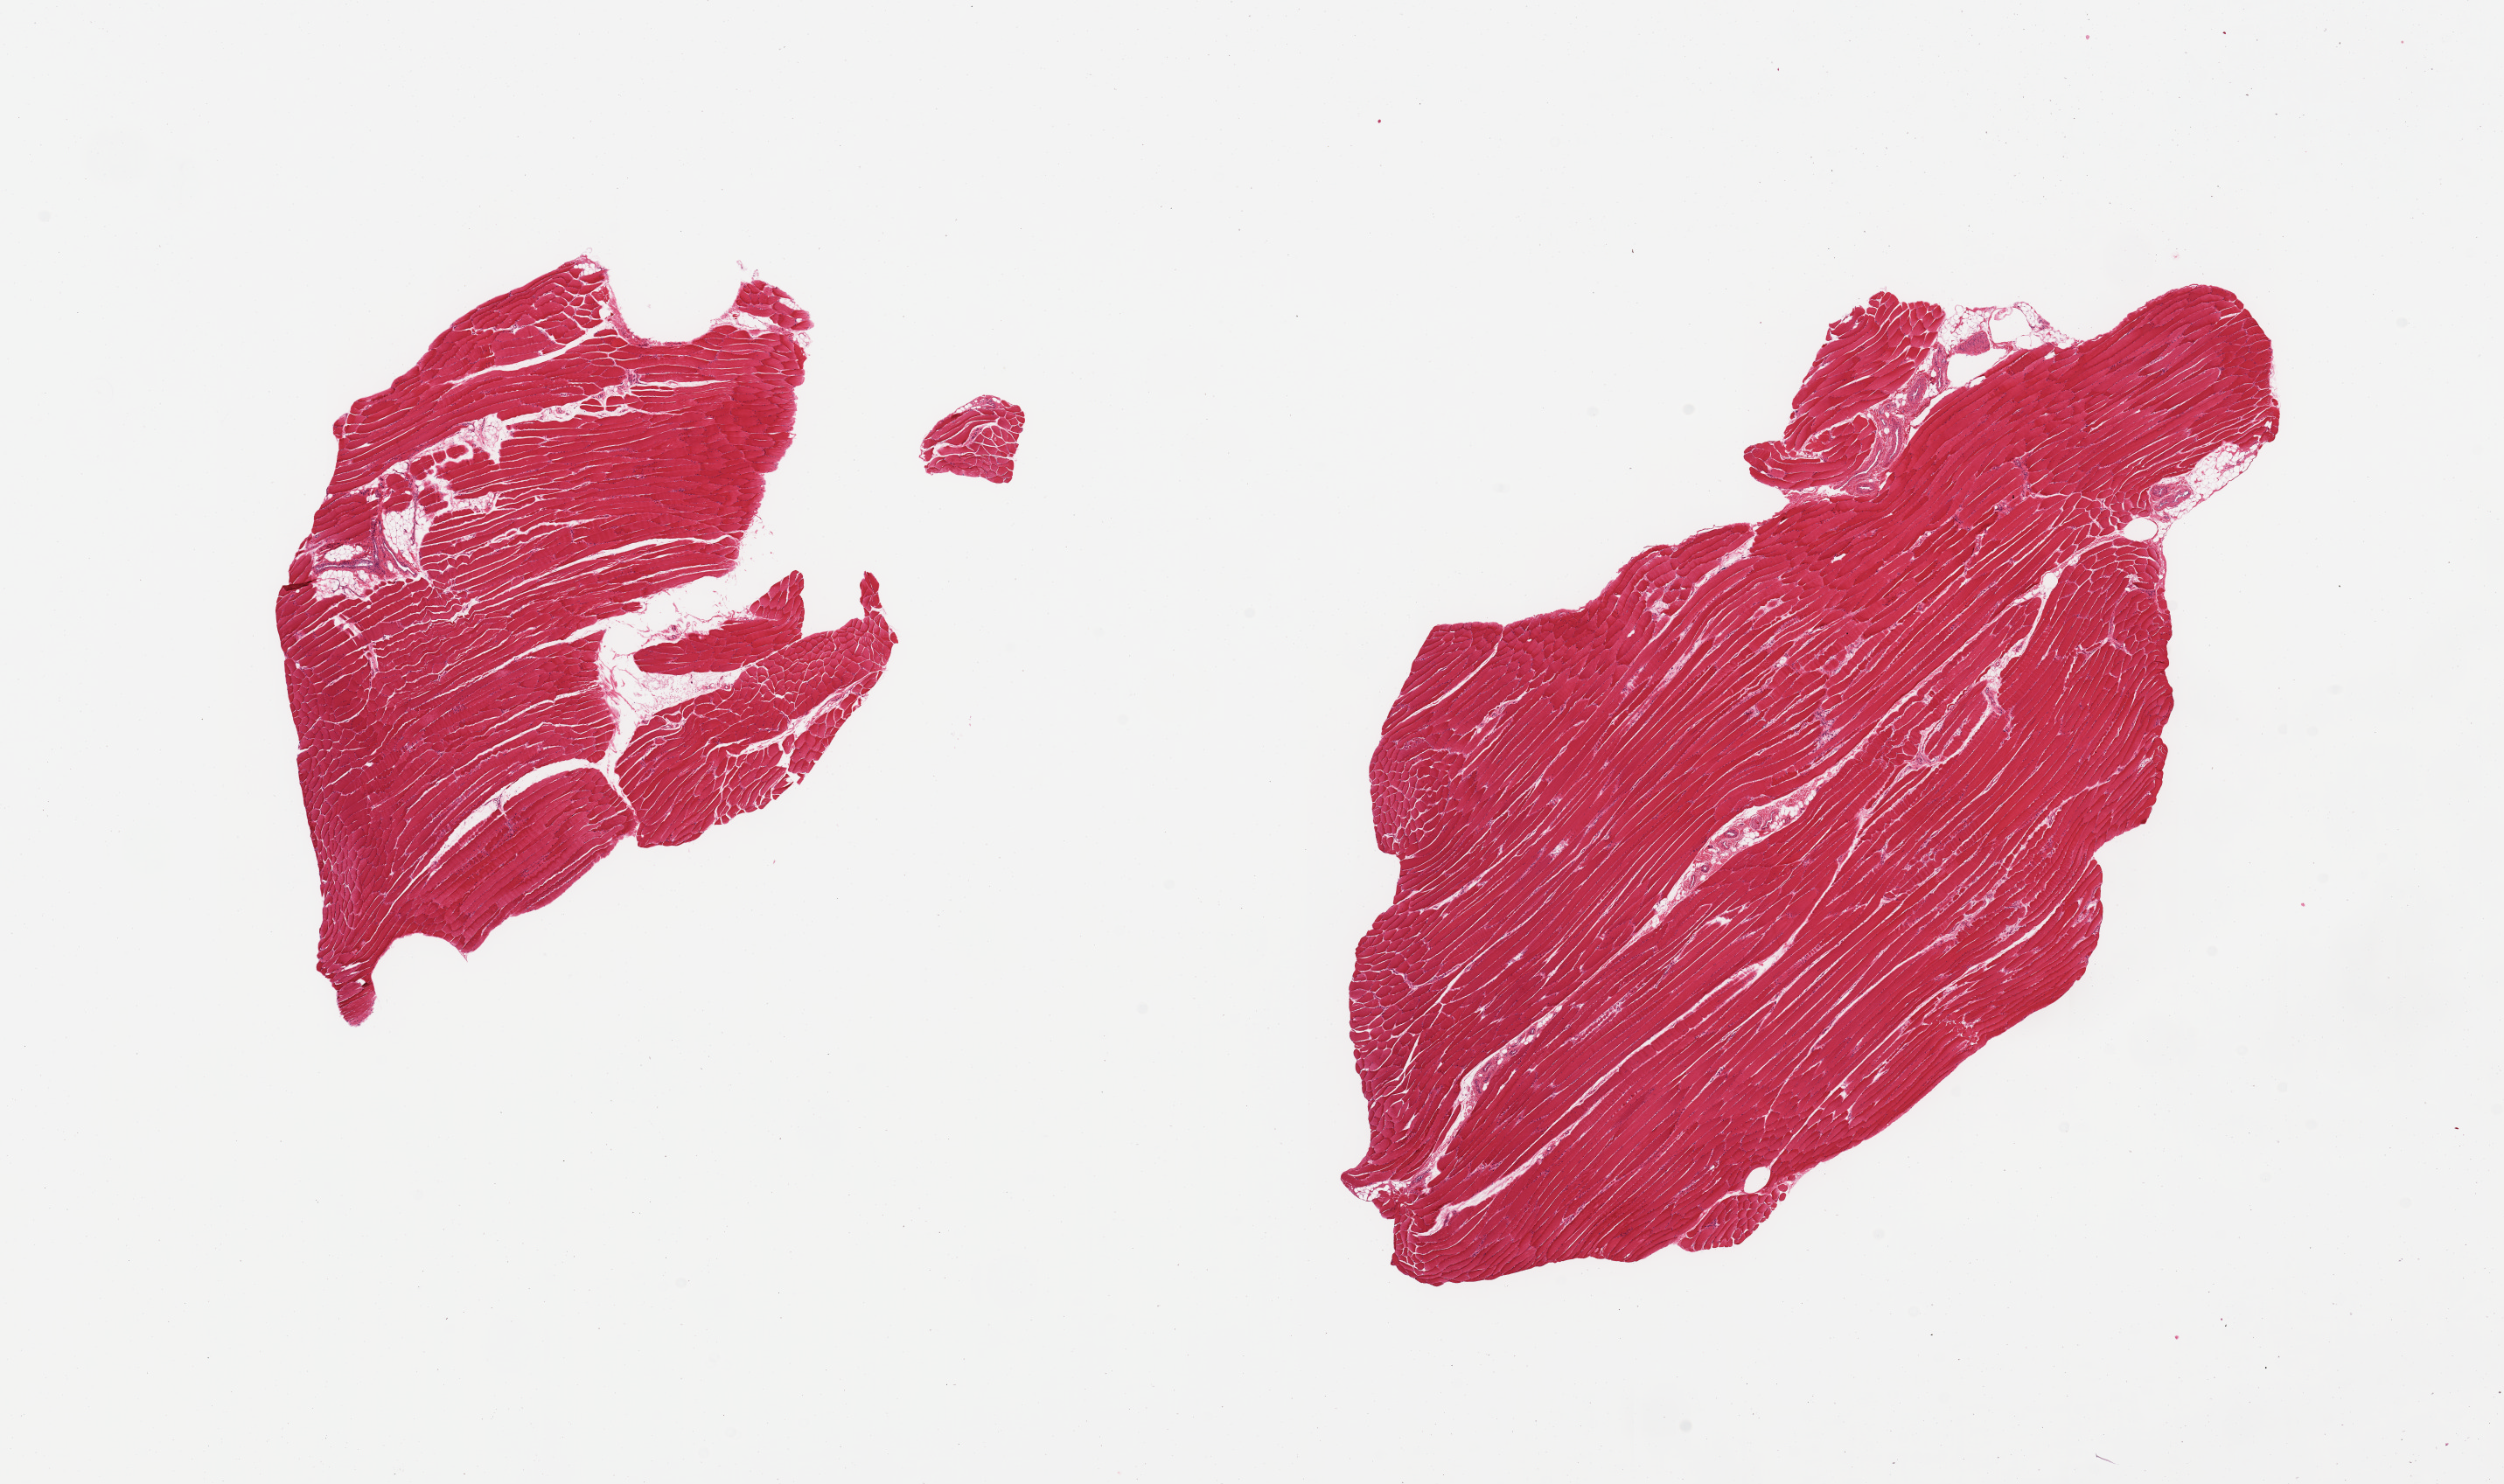
H&E whole-slide image — whole scanned area (about 22.6 x 13.4 mm, from a 20x scan) shown as a low-resolution overview; PAXgene-fixed, paraffin-embedded tissue; section of skeletal muscle (target tissue); donor tissue sample. Donor: female.
Review note (as recorded): 2 pieces; skeletal muscle, <10% is fat/vessels.